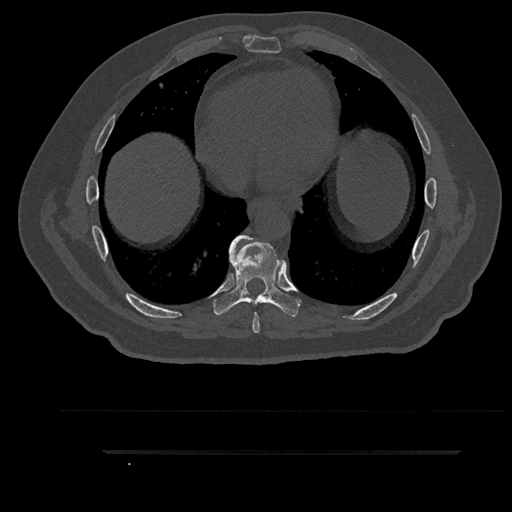
CT including the spine, one axial slice; position 490 of 797 along the scan axis; reconstruction kernel Br40s/3; 120 kVp; bone window (W 1800 / L 400 HU); 0.5 mm slice thickness; 512 × 512 image matrix, field of view 432 × 432 mm. Patient: male, 63 years. From the clinical record (not read from this slice): primary cancer: renal; vertebrae with lytic lesions (as recorded): T8.
Structures marked on this image (semi-automatic segmentation, software-assisted and operator-edited):
- T7 vertebra: bounding box [x1, y1, x2, y2] px = [240, 241, 260, 334]
- T8 vertebra: [212, 235, 300, 317]